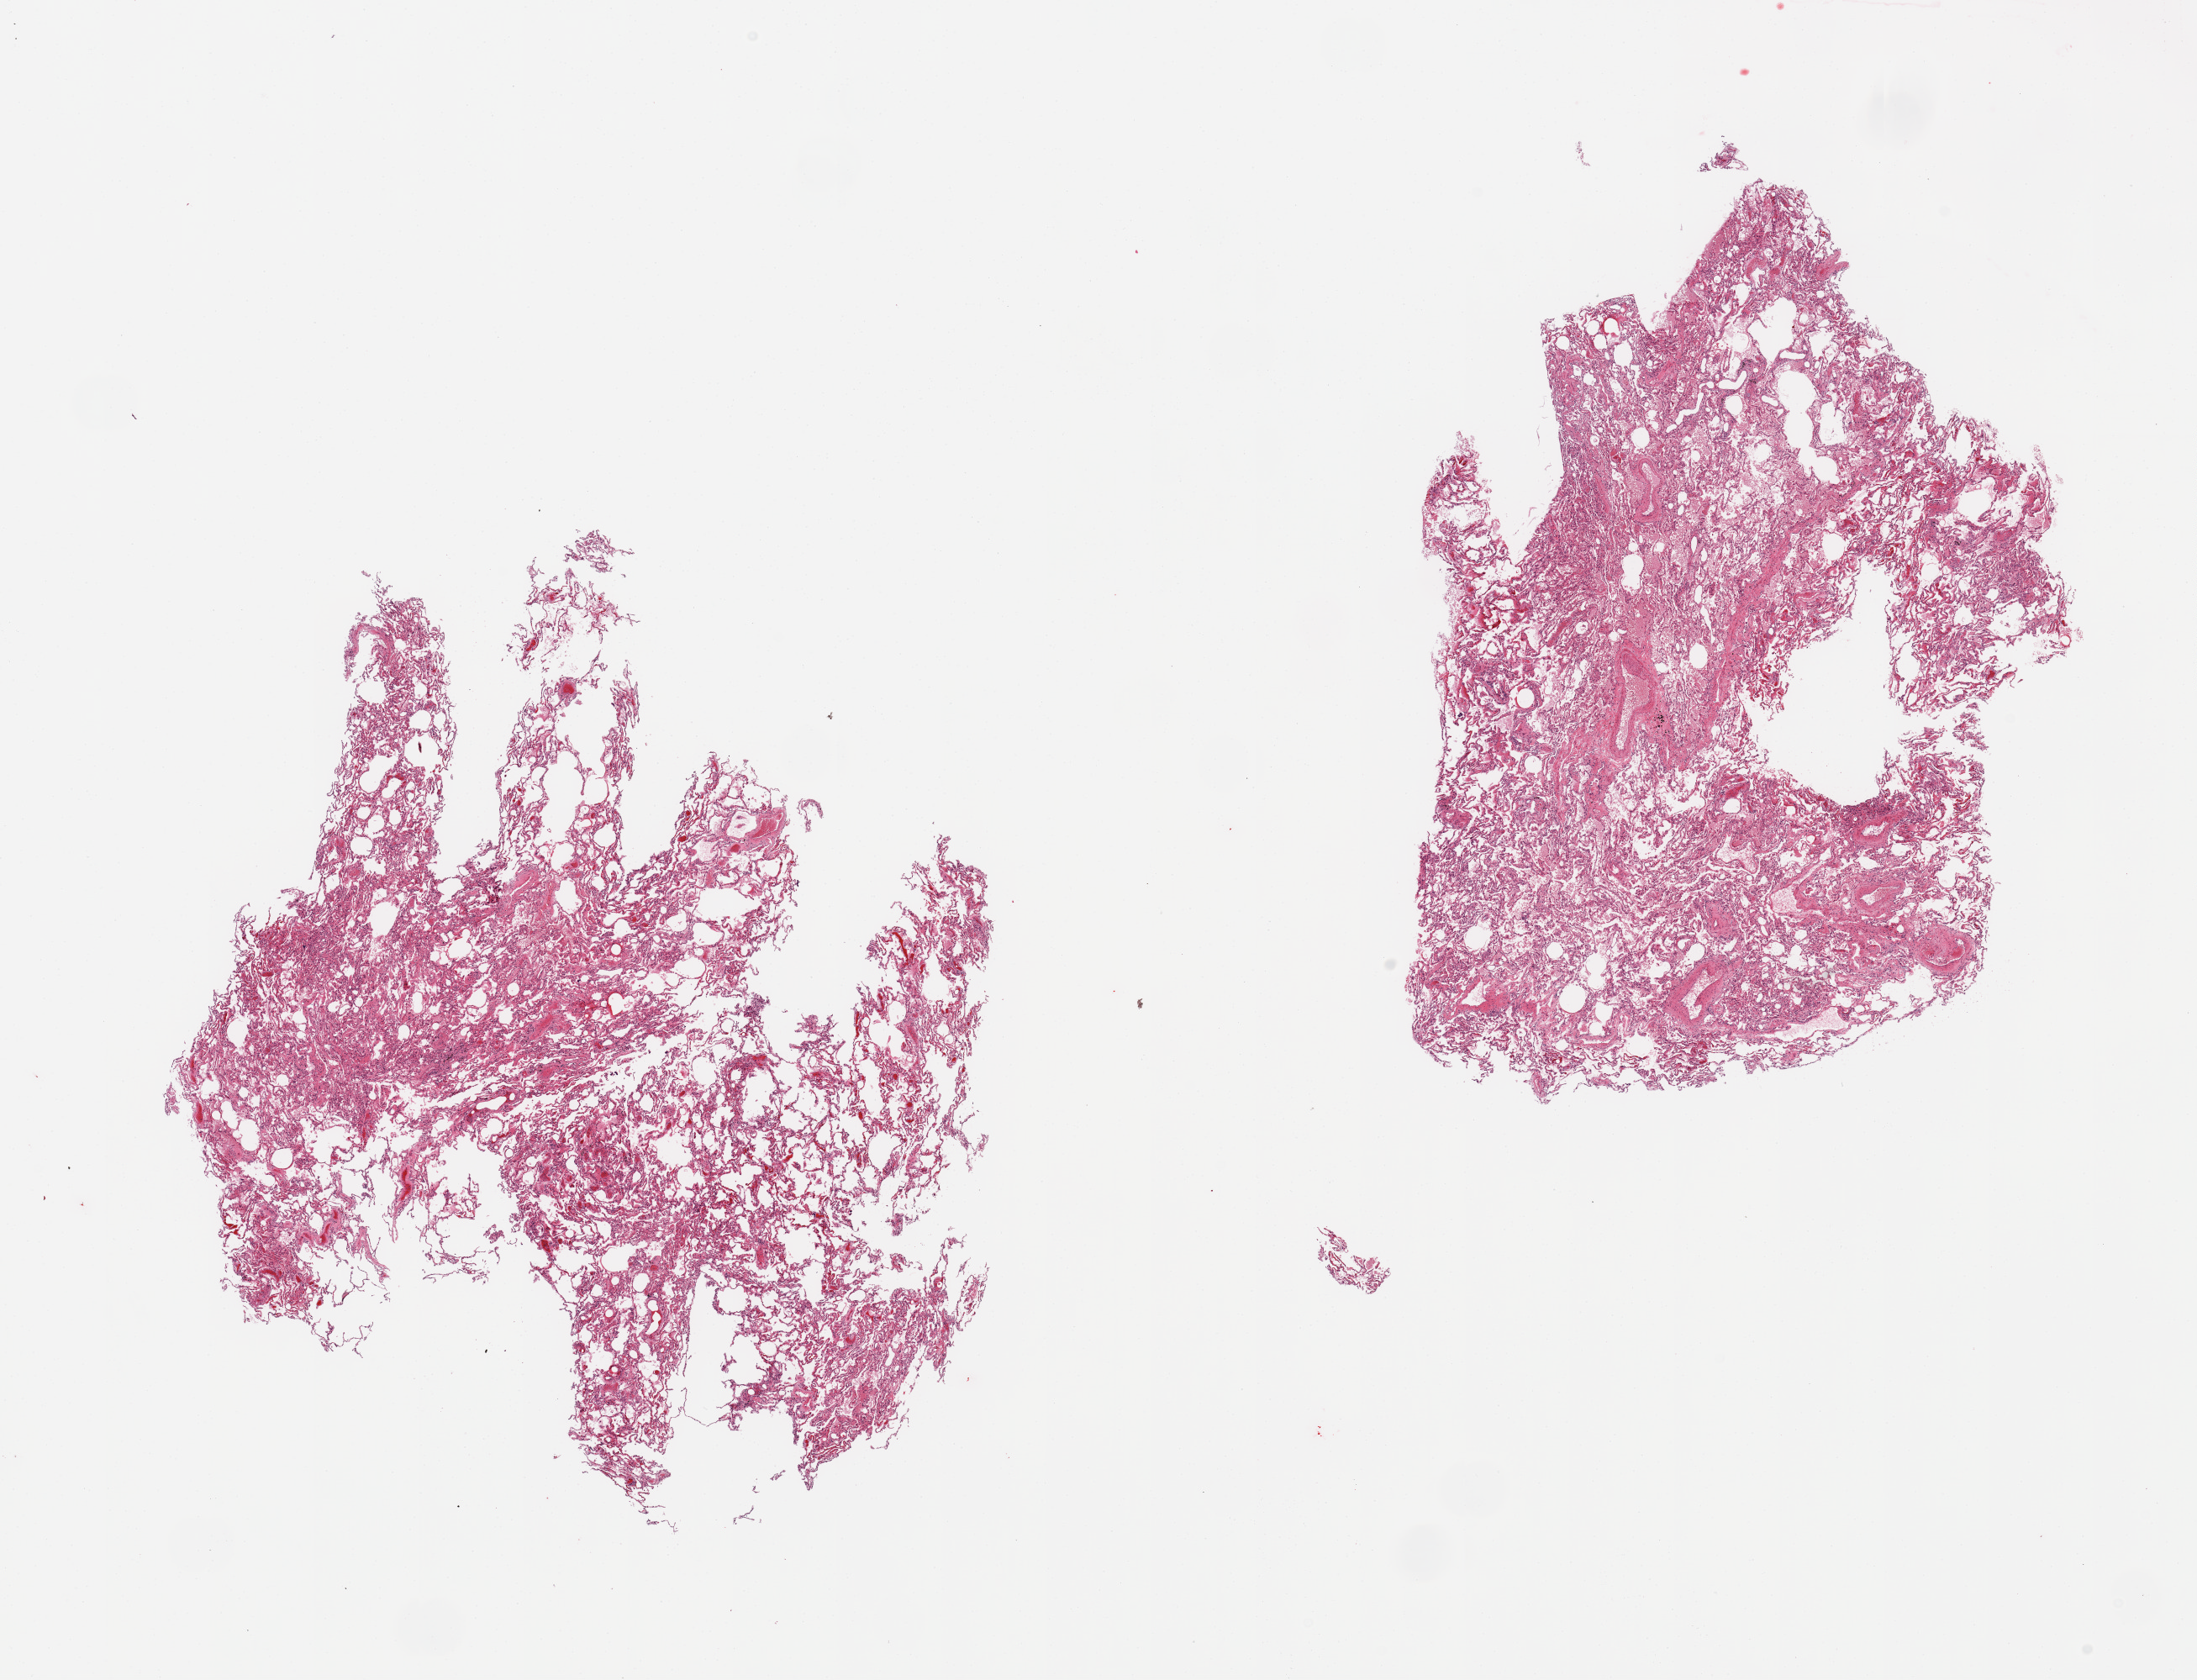
Hematoxylin and eosin (H&E) whole-slide image, brightfield, a low-resolution overview of the entire scanned area, about 20.7 x 15.8 mm (from a 20x scan). PAXgene-fixed, paraffin-embedded tissue. Section of lung (target tissue). Donor tissue sample. Donor sex: male.
* pathologist's review note for this sample: 2 pieces, mild congestion